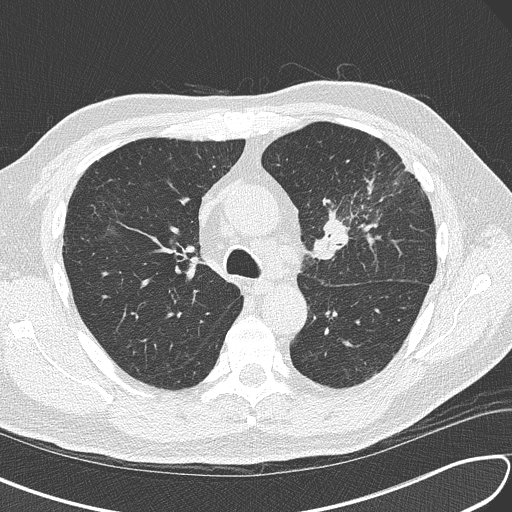
Axial slice from a low-dose chest CT screening exam. Third annual screen. Lung window (W 1500 / L -600 HU). Lung (sharp) reconstruction kernel (B50f). 120 kVp. Slice 52 of 156 in the series. Male, age 67 years at enrolment. Current smoker at enrolment.
Lesion marked by an expert reader, bounding box <299,177,400,273> (left, top, right, bottom; pixels). Reader record for this screening exam (exam-level; its link to the box is not recorded): non-calcified nodule or mass ≥4 mm, left upper lobe, 30 × 23 mm, soft tissue attenuation, pre-existing on the prior screen: no. Official screen result: positive, other. Later outcome: lung cancer diagnosed 41 days after this screen — small cell carcinoma, NOS, left upper lobe, stage IV (AJCC 6th edition), 30 mm at pathology.